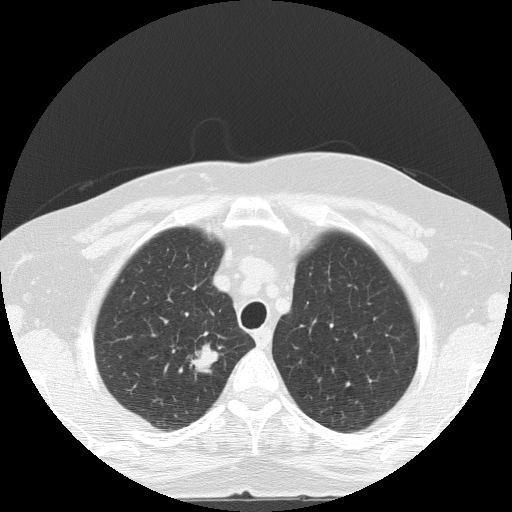
Low-dose screening chest CT, one axial slice; slice 110 of 133 in the series (ordered by position); lung window (W 1500 / L -600 HU); 512 × 512 image matrix, field of view 320 × 320 mm.
Structures marked on this image (manually delineated by an expert):
- lesion 1 (tumor, upper lobe of right lung): bounding box (x1, y1, x2, y2) in pixels: (190, 344, 223, 373)